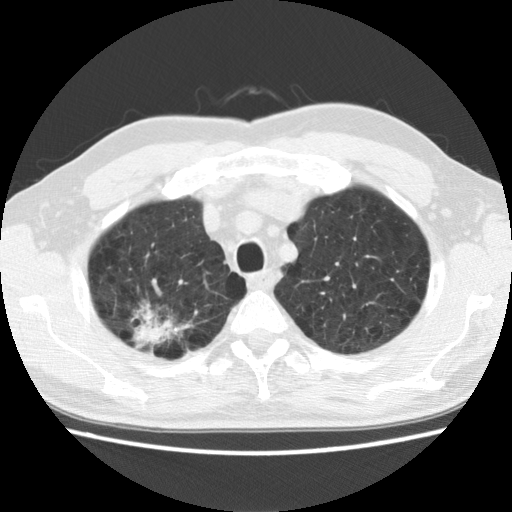
Low-dose screening chest CT, one axial slice. Slice 114 of 142 in the series (ordered by position). 120 kVp. Lung window (W 1500 / L -600 HU). 2.5 mm slice thickness. 512 × 512 image matrix.
Annotated regions visible in this slice (expert manual segmentation):
- lesion 1 (tumor, upper lobe of right lung): bounding box <137,321,164,346> (left, top, right, bottom; pixels)